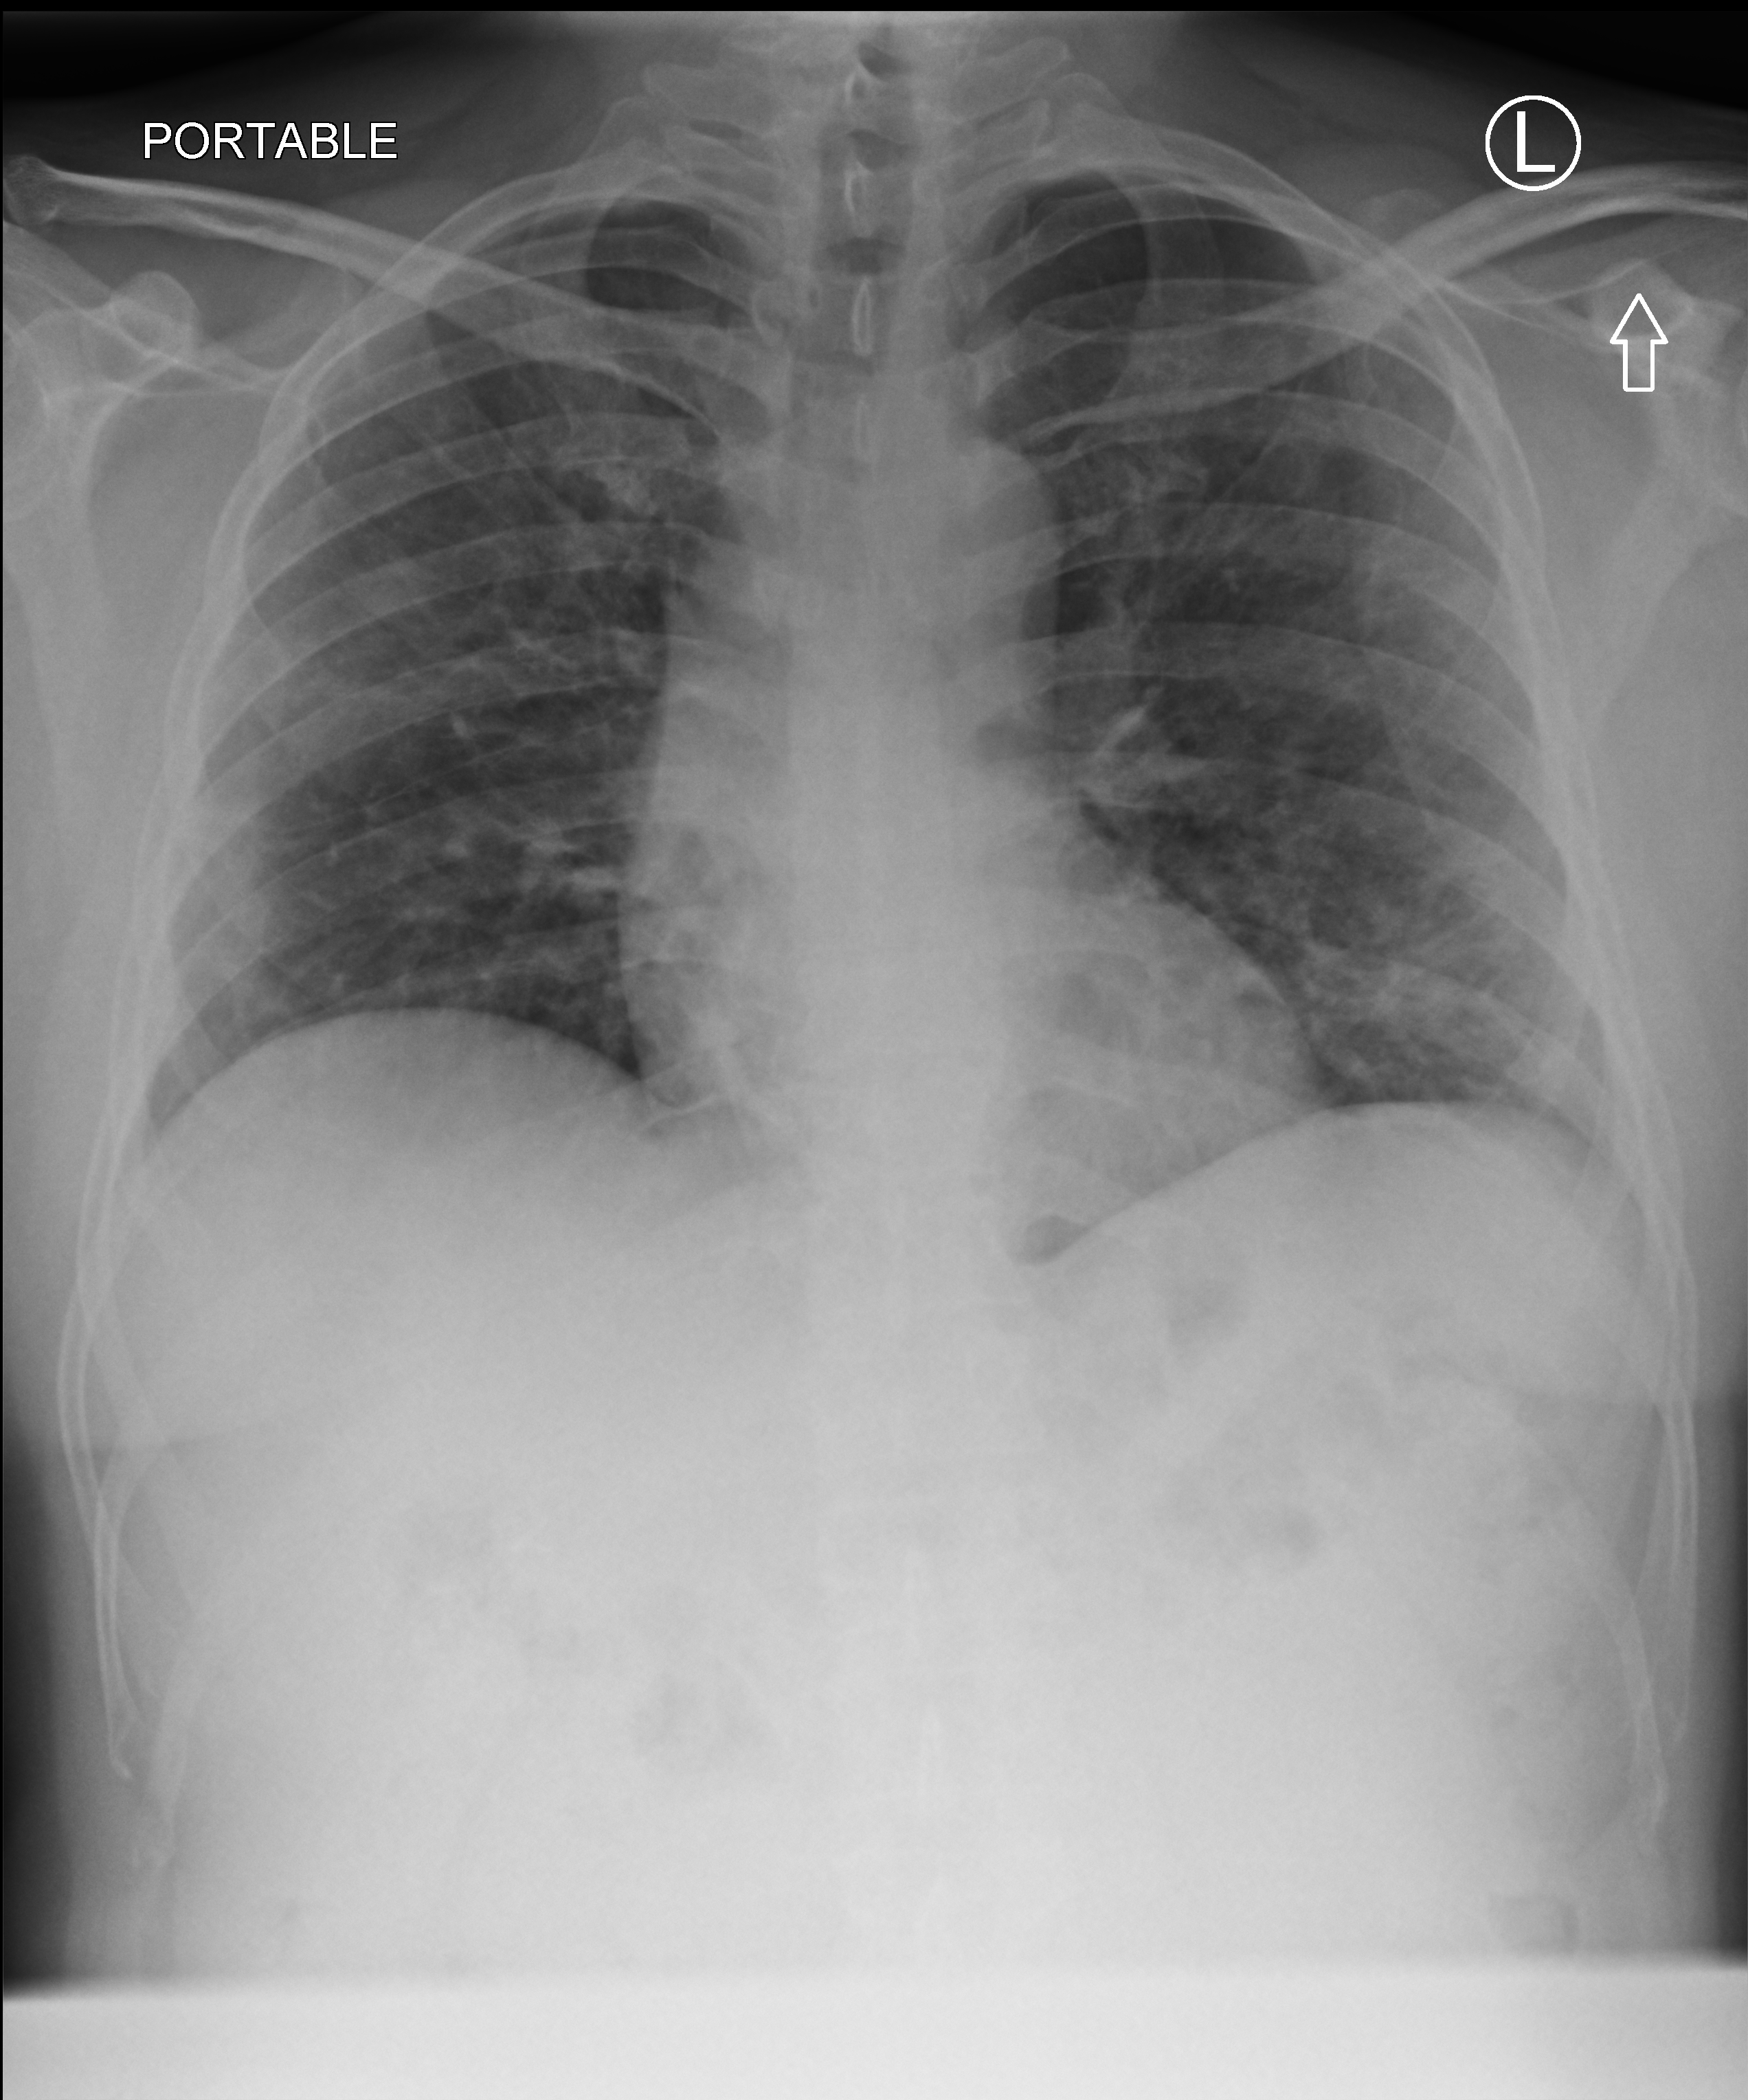
Portable chest radiograph. Male patient hospitalised with COVID-19, age 18–59 years.
Hospital-stay facts (about this admission, not read from this image; timing relative to this image not recorded): mechanically ventilated during this hospital stay: no.